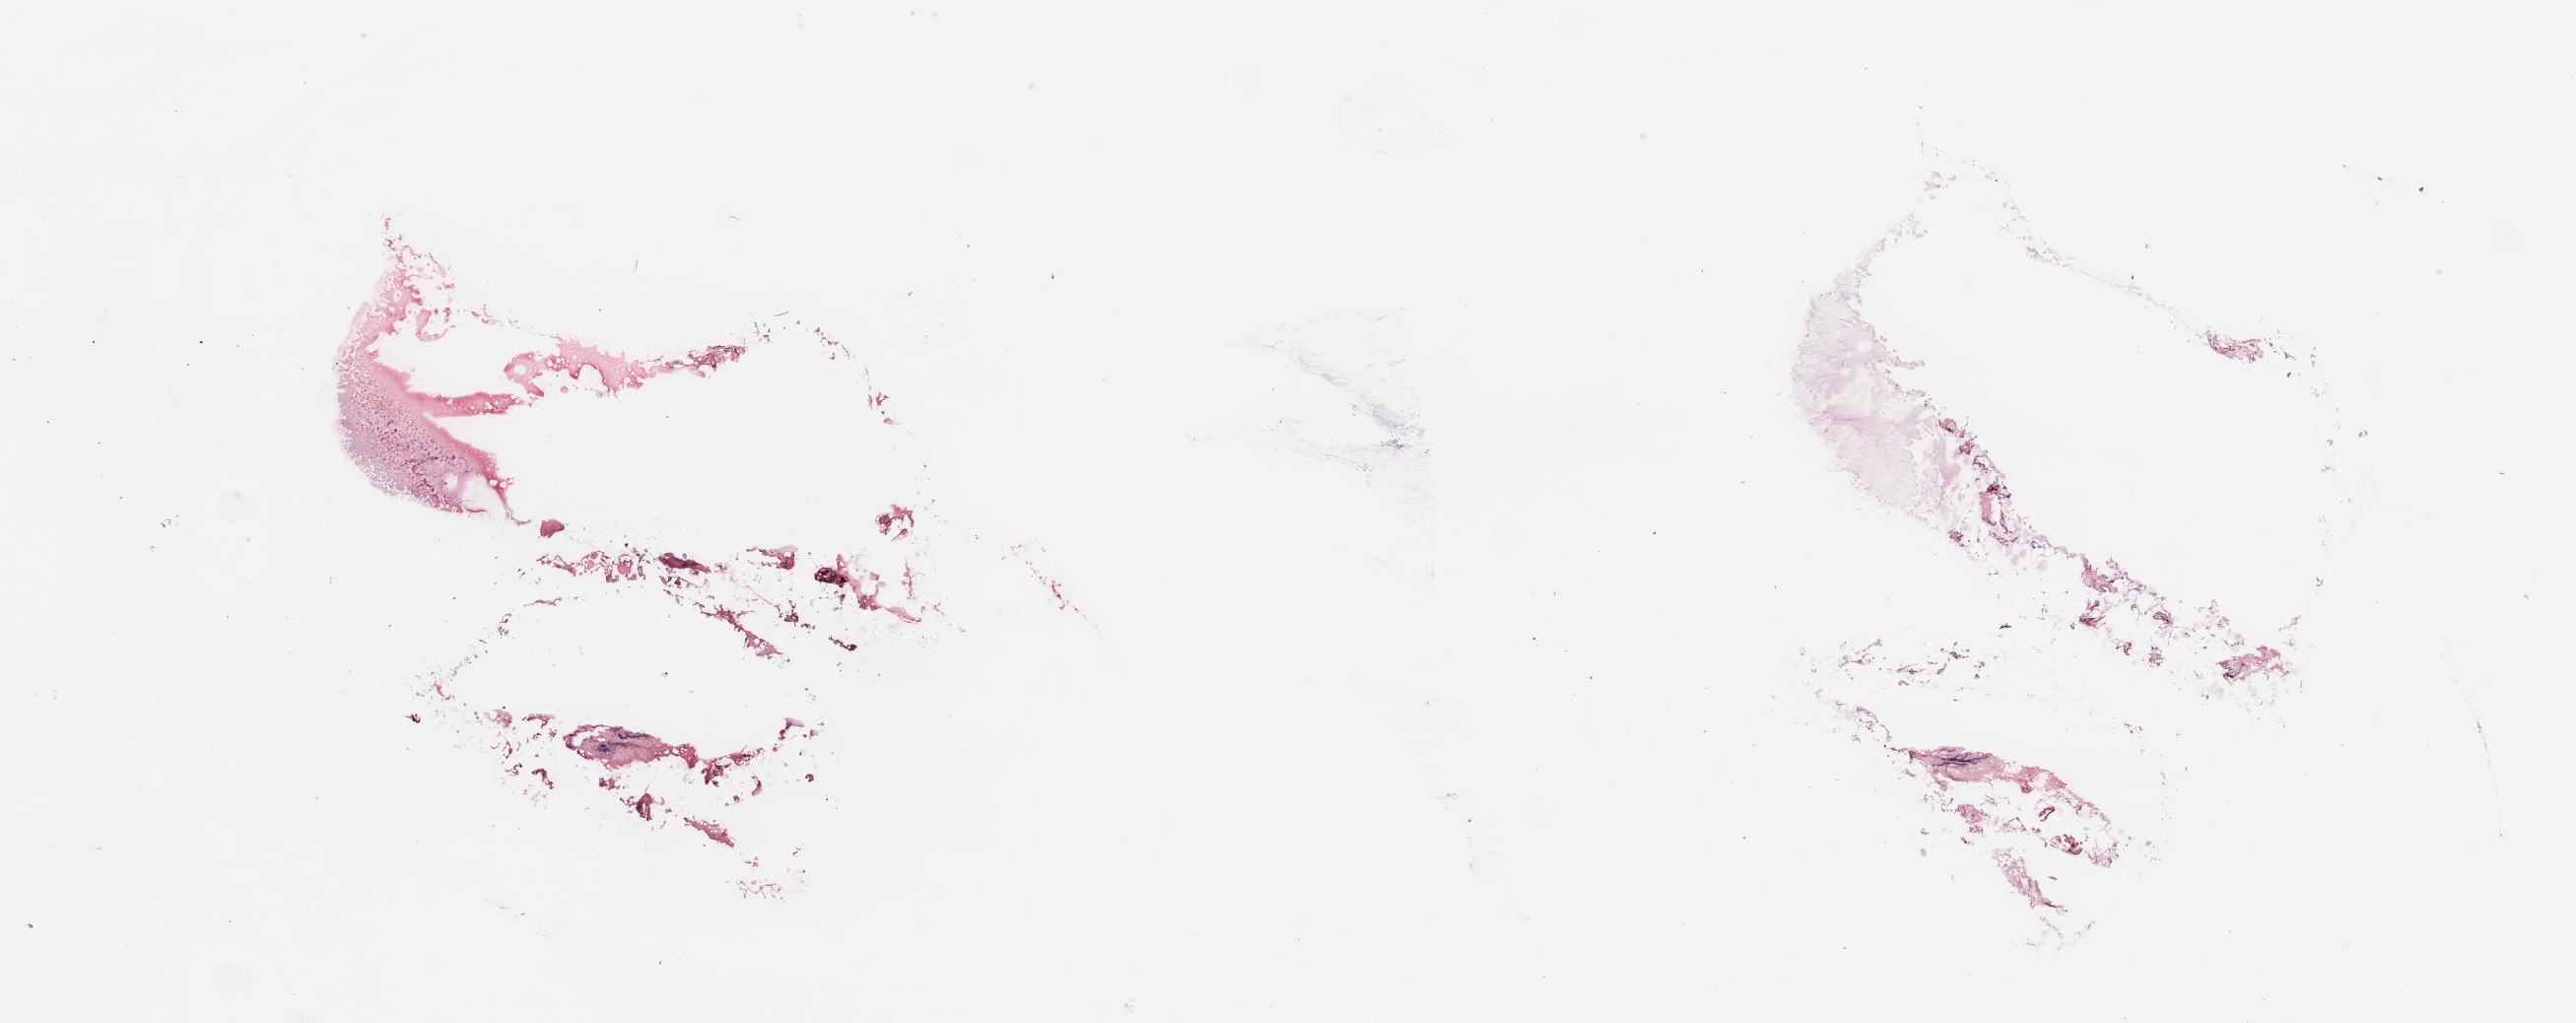
Whole-slide histology image, Hematoxylin and eosin (H&E) stained — shown as a low-resolution overview of the whole scanned area (about 41.3 x 16.4 mm, acquisition: 20x scan), breast, tissue type not recorded.
Patient diagnosis (cohort enrolment): breast cancer (breast).